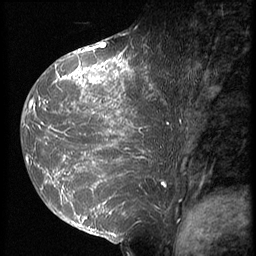
Breast MRI (dynamic contrast-enhanced), one sagittal slice; position 33 of 64 along the scan axis; 3 images stored at this slice position (order not interpretable as contrast timing); 1.5 T; TE 4.2 ms, TR 9 ms; 256 × 256 image matrix, field of view 180 × 180 mm. Patient: female, 39 years. Case-level facts recorded for this patient, not image findings: setting: breast cancer imaged before/during neoadjuvant chemotherapy; receptor status: HER2-positive.
Annotated regions visible in this slice (semi-automatically segmented with operator editing):
- analysis volume of interest (the breast-tissue region the enhancement analysis was run in; not a lesion): bounding box (x1, y1, x2, y2) in pixels: (23, 47, 171, 239)
- tumour enhancement mask (voxels above the 140 % enhancement threshold inside the analysis volume of interest): (23, 47, 164, 234)